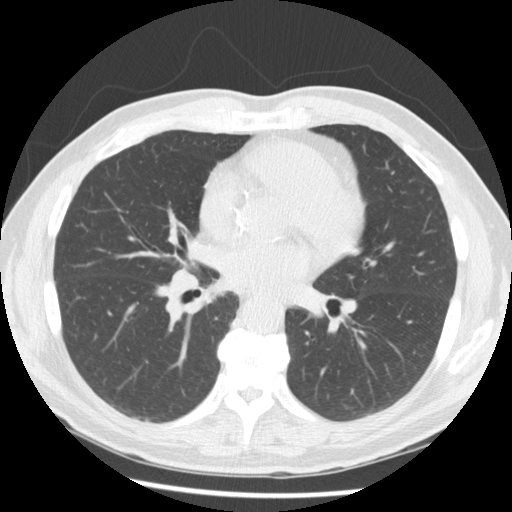
Low-dose screening chest CT, axial slice, baseline screening round, lung window (W 1500 / L -600 HU), 120 kVp, 512 × 512 image matrix. Male participant, aged 62 years at enrolment. Current smoker at enrolment.
Expert reader's lesion annotation, bounding box [x1, y1, x2, y2] px = [154, 252, 216, 310]. Screening reader's record for this exam: no non-calcified nodule ≥4 mm recorded. Lung cancer was diagnosed 146 days after this screen: small cell carcinoma, NOS, right hilum, mediastinum, poorly differentiated (G3), stage IV (AJCC 6th edition).